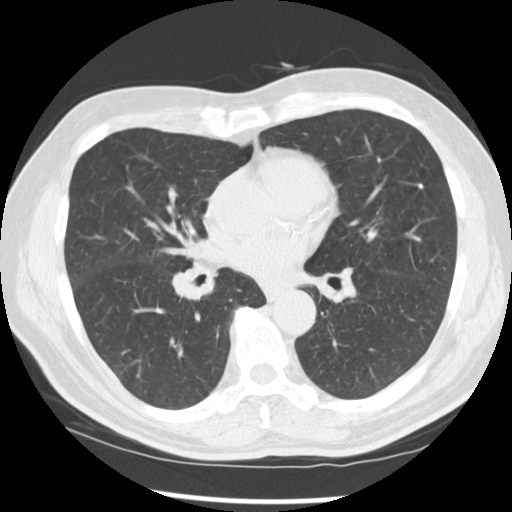
Axial slice from a low-dose chest CT screening exam; baseline annual screen; lung window (W 1500 / L -600 HU); 2.5 mm slice thickness; standard (soft-tissue) reconstruction kernel (STANDARD); 120 kVp; 512 × 512 image matrix, field of view 365 × 365 mm. Male, age 67 years at enrolment. Current smoker at enrolment.
• Lesion marked by an expert reader, bounding box (x1, y1, x2, y2) in pixels: (156, 245, 228, 313).
• Screening reader's record for this exam (one nodule recorded; not confirmed to be the boxed lesion): non-calcified nodule or mass ≥4 mm, left lower lobe, 15 × 15 mm, spiculated (stellate) margins, soft tissue attenuation.
• Note: the box lies in the patient's right hemithorax on this image, whereas the reader's record names the left lung; they may be different findings.
• Later outcome: lung cancer diagnosed 49 days after this screen — squamous cell carcinoma, NOS, right middle lobe, poorly differentiated (G3), stage IIB (AJCC 6th edition), 35 mm at pathology.